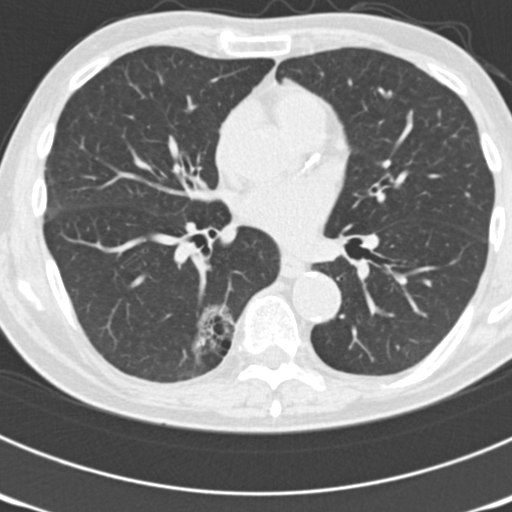
Axial slice from a low-dose chest CT screening exam, third screening round (two years after baseline), lung window (W 1500 / L -600 HU), 2 mm slice thickness, standard (soft-tissue) reconstruction kernel (B30f), slice 84 of 177 in the series. Male participant, aged 70 years at enrolment. Current smoker at enrolment.
Expert-annotated lung lesion, bounding box <148,301,238,384> (left, top, right, bottom; pixels). The screening reader recorded 3 non-calcified nodules or masses ≥4 mm on this exam; which of them this box marks is not recorded. Later outcome: lung cancer diagnosed 14 days after this screen — bronchiolo-alveolar adenocarcinoma, NOS, right lower lobe, poorly differentiated (G3), stage IB (AJCC 6th edition), 30 mm at pathology.